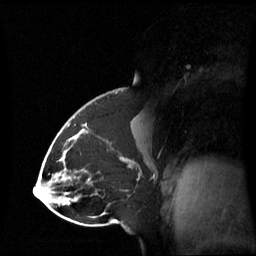
Breast MRI (dynamic contrast-enhanced), one sagittal slice; position 34 of 60 along the scan axis; dynamic contrast-enhanced series, image 2 of 3 at this slice position (ordered by acquisition); 1.5 T; TE 4.2 ms, TR 8.4 ms; 2.8 mm slice thickness; 256 × 256 image matrix, field of view 270 × 270 mm. Patient: female, 43 years. From the clinical record (not read from this slice): setting: breast cancer imaged before/during neoadjuvant chemotherapy; receptor status: triple-negative.
Annotated regions visible in this slice (semi-automatically segmented with operator editing):
- analysis volume of interest (the breast-tissue region the enhancement analysis was run in; not a lesion): bounding box <65,118,143,198> (left, top, right, bottom; pixels)
- tumour enhancement mask (voxels above the 70 % enhancement threshold inside the analysis volume of interest): <67,125,129,180>